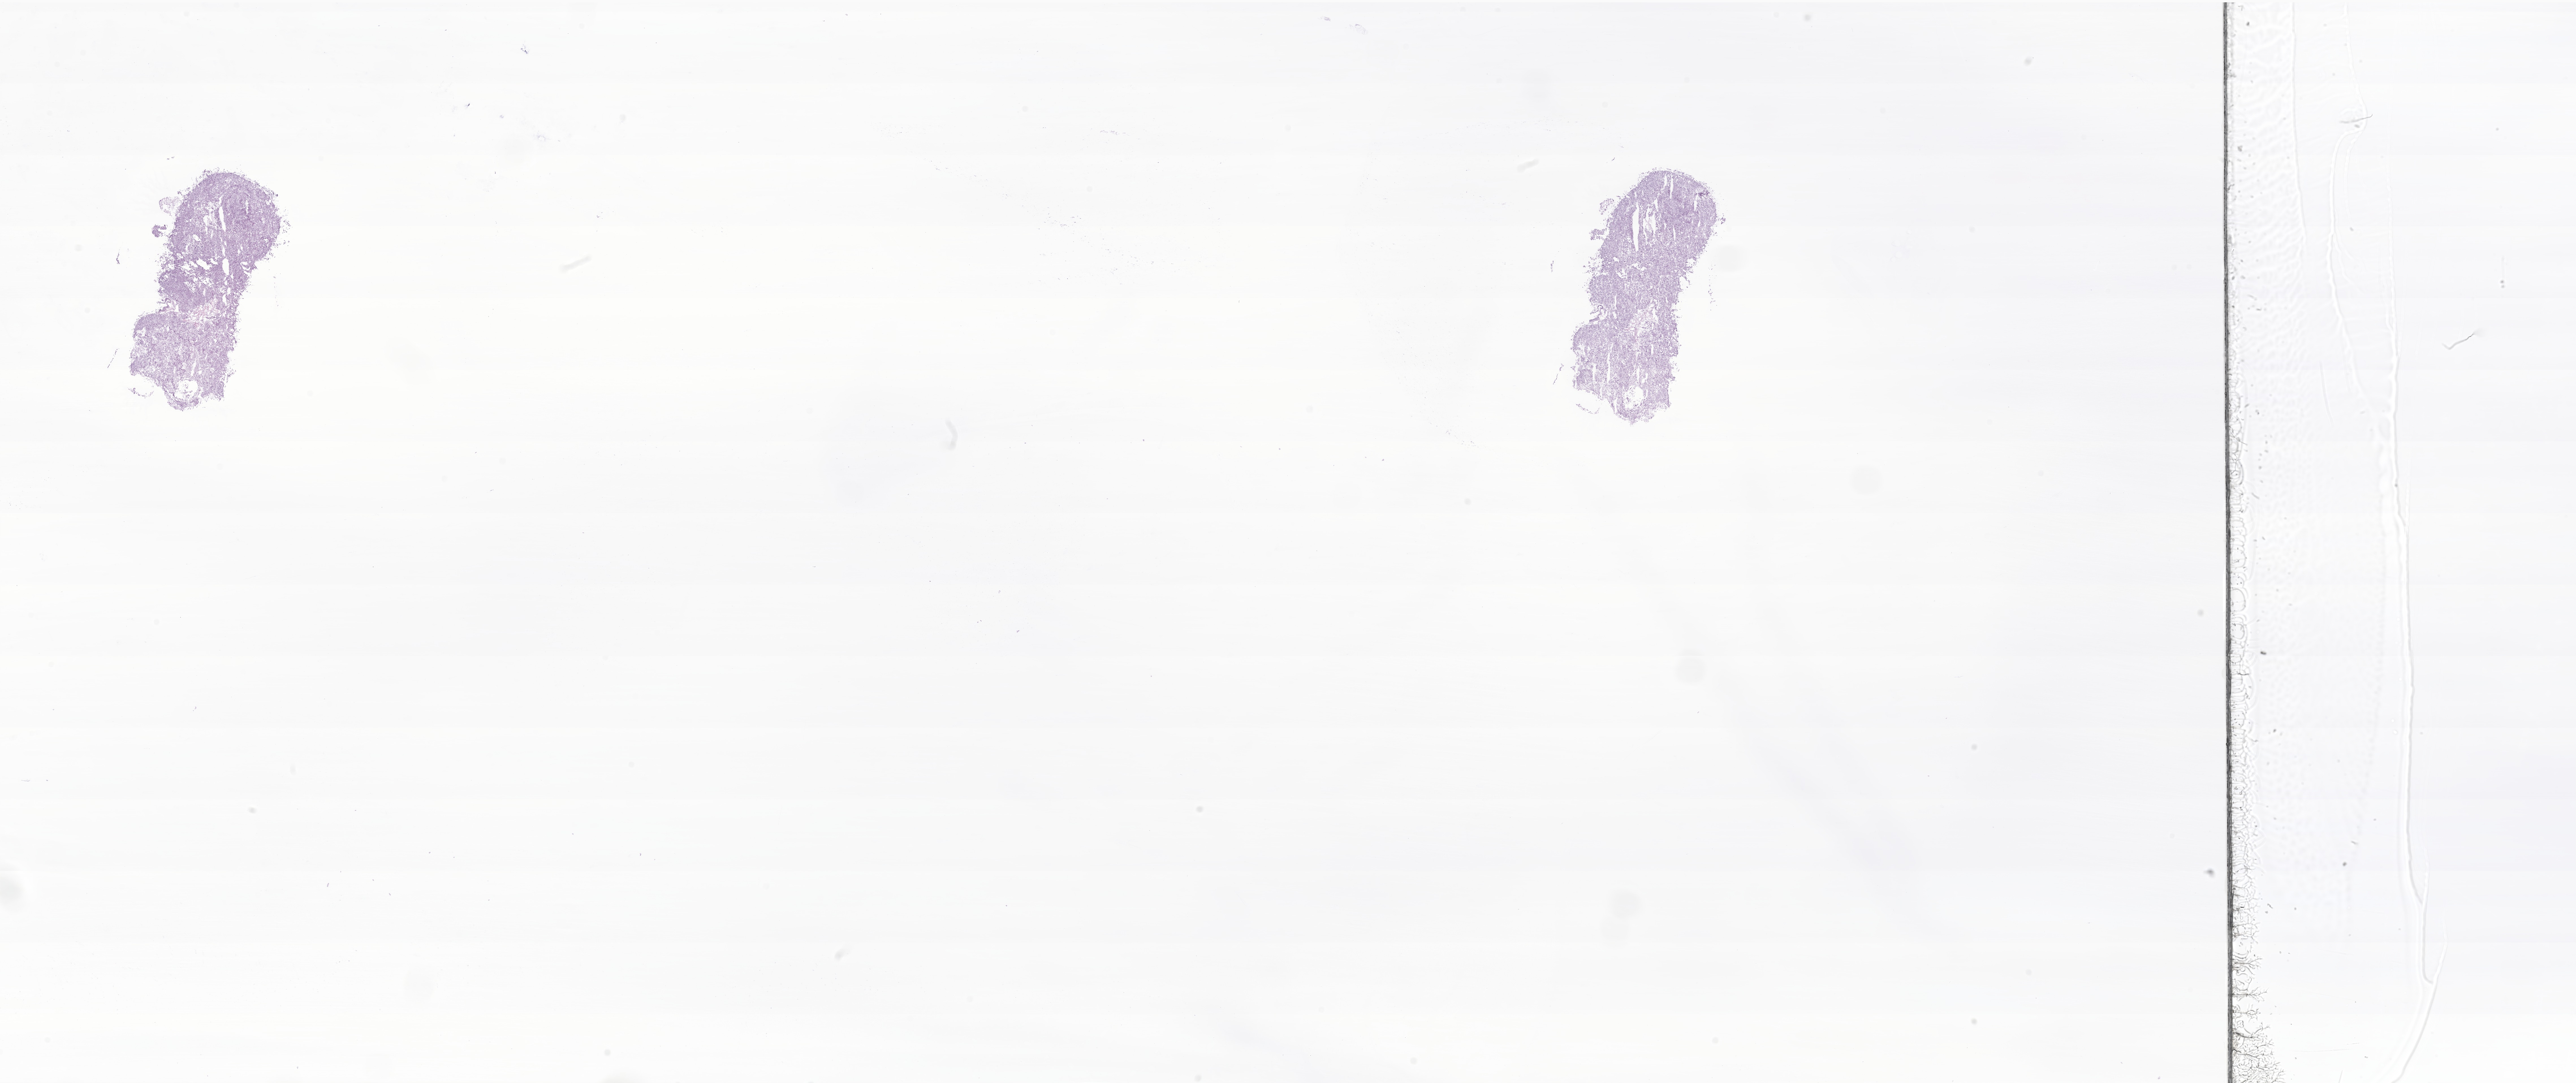
Whole-slide image, H&E stain of tumor tissue from the soft tissue of upper extremity, shown as a low-resolution overview of the whole scanned area (about 38.4 x 16.2 mm); frozen section (OCT-embedded). Patient female; age 179 months.
Recorded diagnosis: Alveolar soft part sarcoma. Tissue or organ of origin (case record): connective, subcutaneous and other soft tissues of upper limb and shoulder.